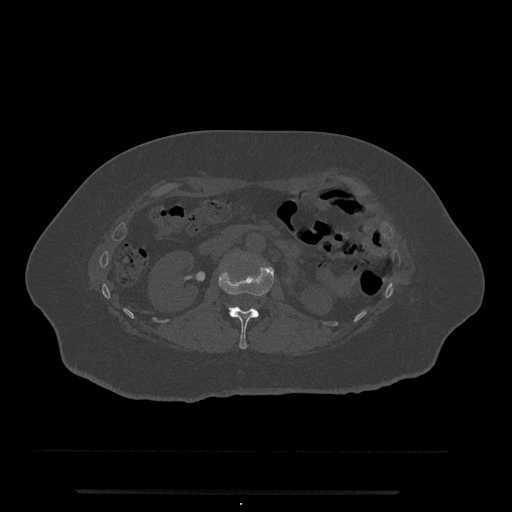
CT including the spine, one axial slice. Slice 87 of 797 in the series (ordered by position). Bone window (W 1800 / L 400 HU). 512 × 512 image matrix, field of view 440 × 440 mm. Female patient, age 51 years. From the clinical record (not read from this slice): primary cancer: neuro; vertebrae with lytic lesions (as recorded): T8.
Structures marked on this image (semi-automatic segmentation, software-assisted and operator-edited):
- L1 vertebra: box from (x=218, y=259) to (x=274, y=350) px
- L2 vertebra: (x=229, y=306)–(x=237, y=311)